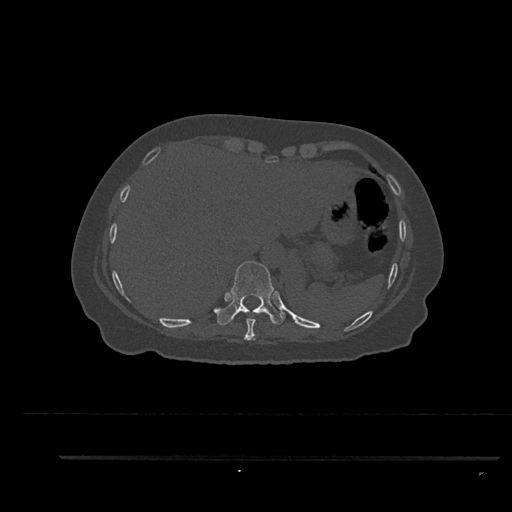
CT including the spine, one axial slice; reconstruction kernel Br40s/3; 120 kVp; bone window (W 1800 / L 400 HU); 512 × 512 image matrix, field of view 408 × 408 mm. Patient: female, 44 years. From the clinical record (not read from this slice): primary cancer: renal.
Outlined on this slice (semi-automatically segmented with operator editing):
- T10 vertebra: bounding box [x1, y1, x2, y2] px = [217, 261, 284, 325]
- T9 vertebra: [244, 318, 256, 340]